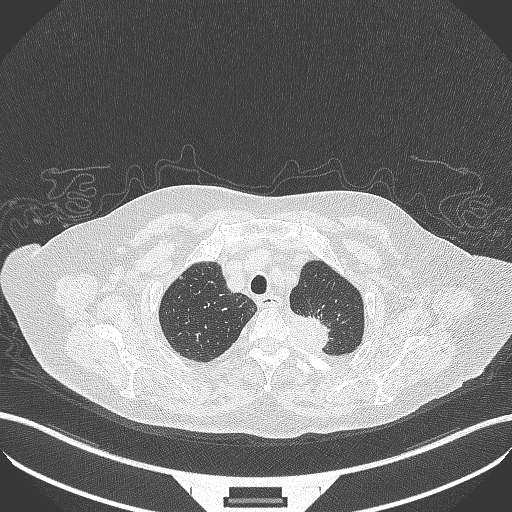
Chest CT, one axial slice; slice 295 of 353 in the series (ordered by position); reconstruction kernel B70f; lung window (W 1500 / L -600 HU); 1 mm slice thickness; 512 × 512 image matrix, field of view 400 × 400 mm. Patient: female, 81 years. Case-level facts recorded for this patient, not image findings: clinical TNM (as recorded): T2a N0 M0.
Outlined on this slice (rectangle marked by the reading radiologist):
- lung tumour (recorded histology: adenocarcinoma): box from (x=288, y=308) to (x=332, y=354) px